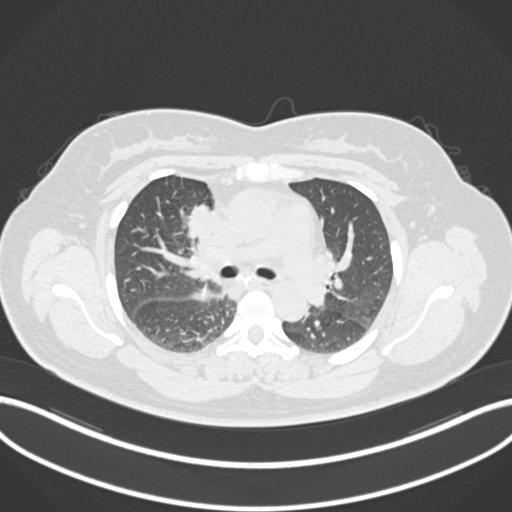
Chest CT, one axial slice; slice 111 of 183 in the series (ordered by position); lung window (W 1500 / L -600 HU); 512 × 512 image matrix, field of view 400 × 400 mm. Female patient, age 46 years. Case-level facts recorded for this patient, not image findings: clinical TNM (as recorded): T2a N1 M0.
Structures marked on this image (rectangle marked by the reading radiologist):
- lung tumour (recorded histology: adenocarcinoma): box from (x=187, y=199) to (x=215, y=246) px